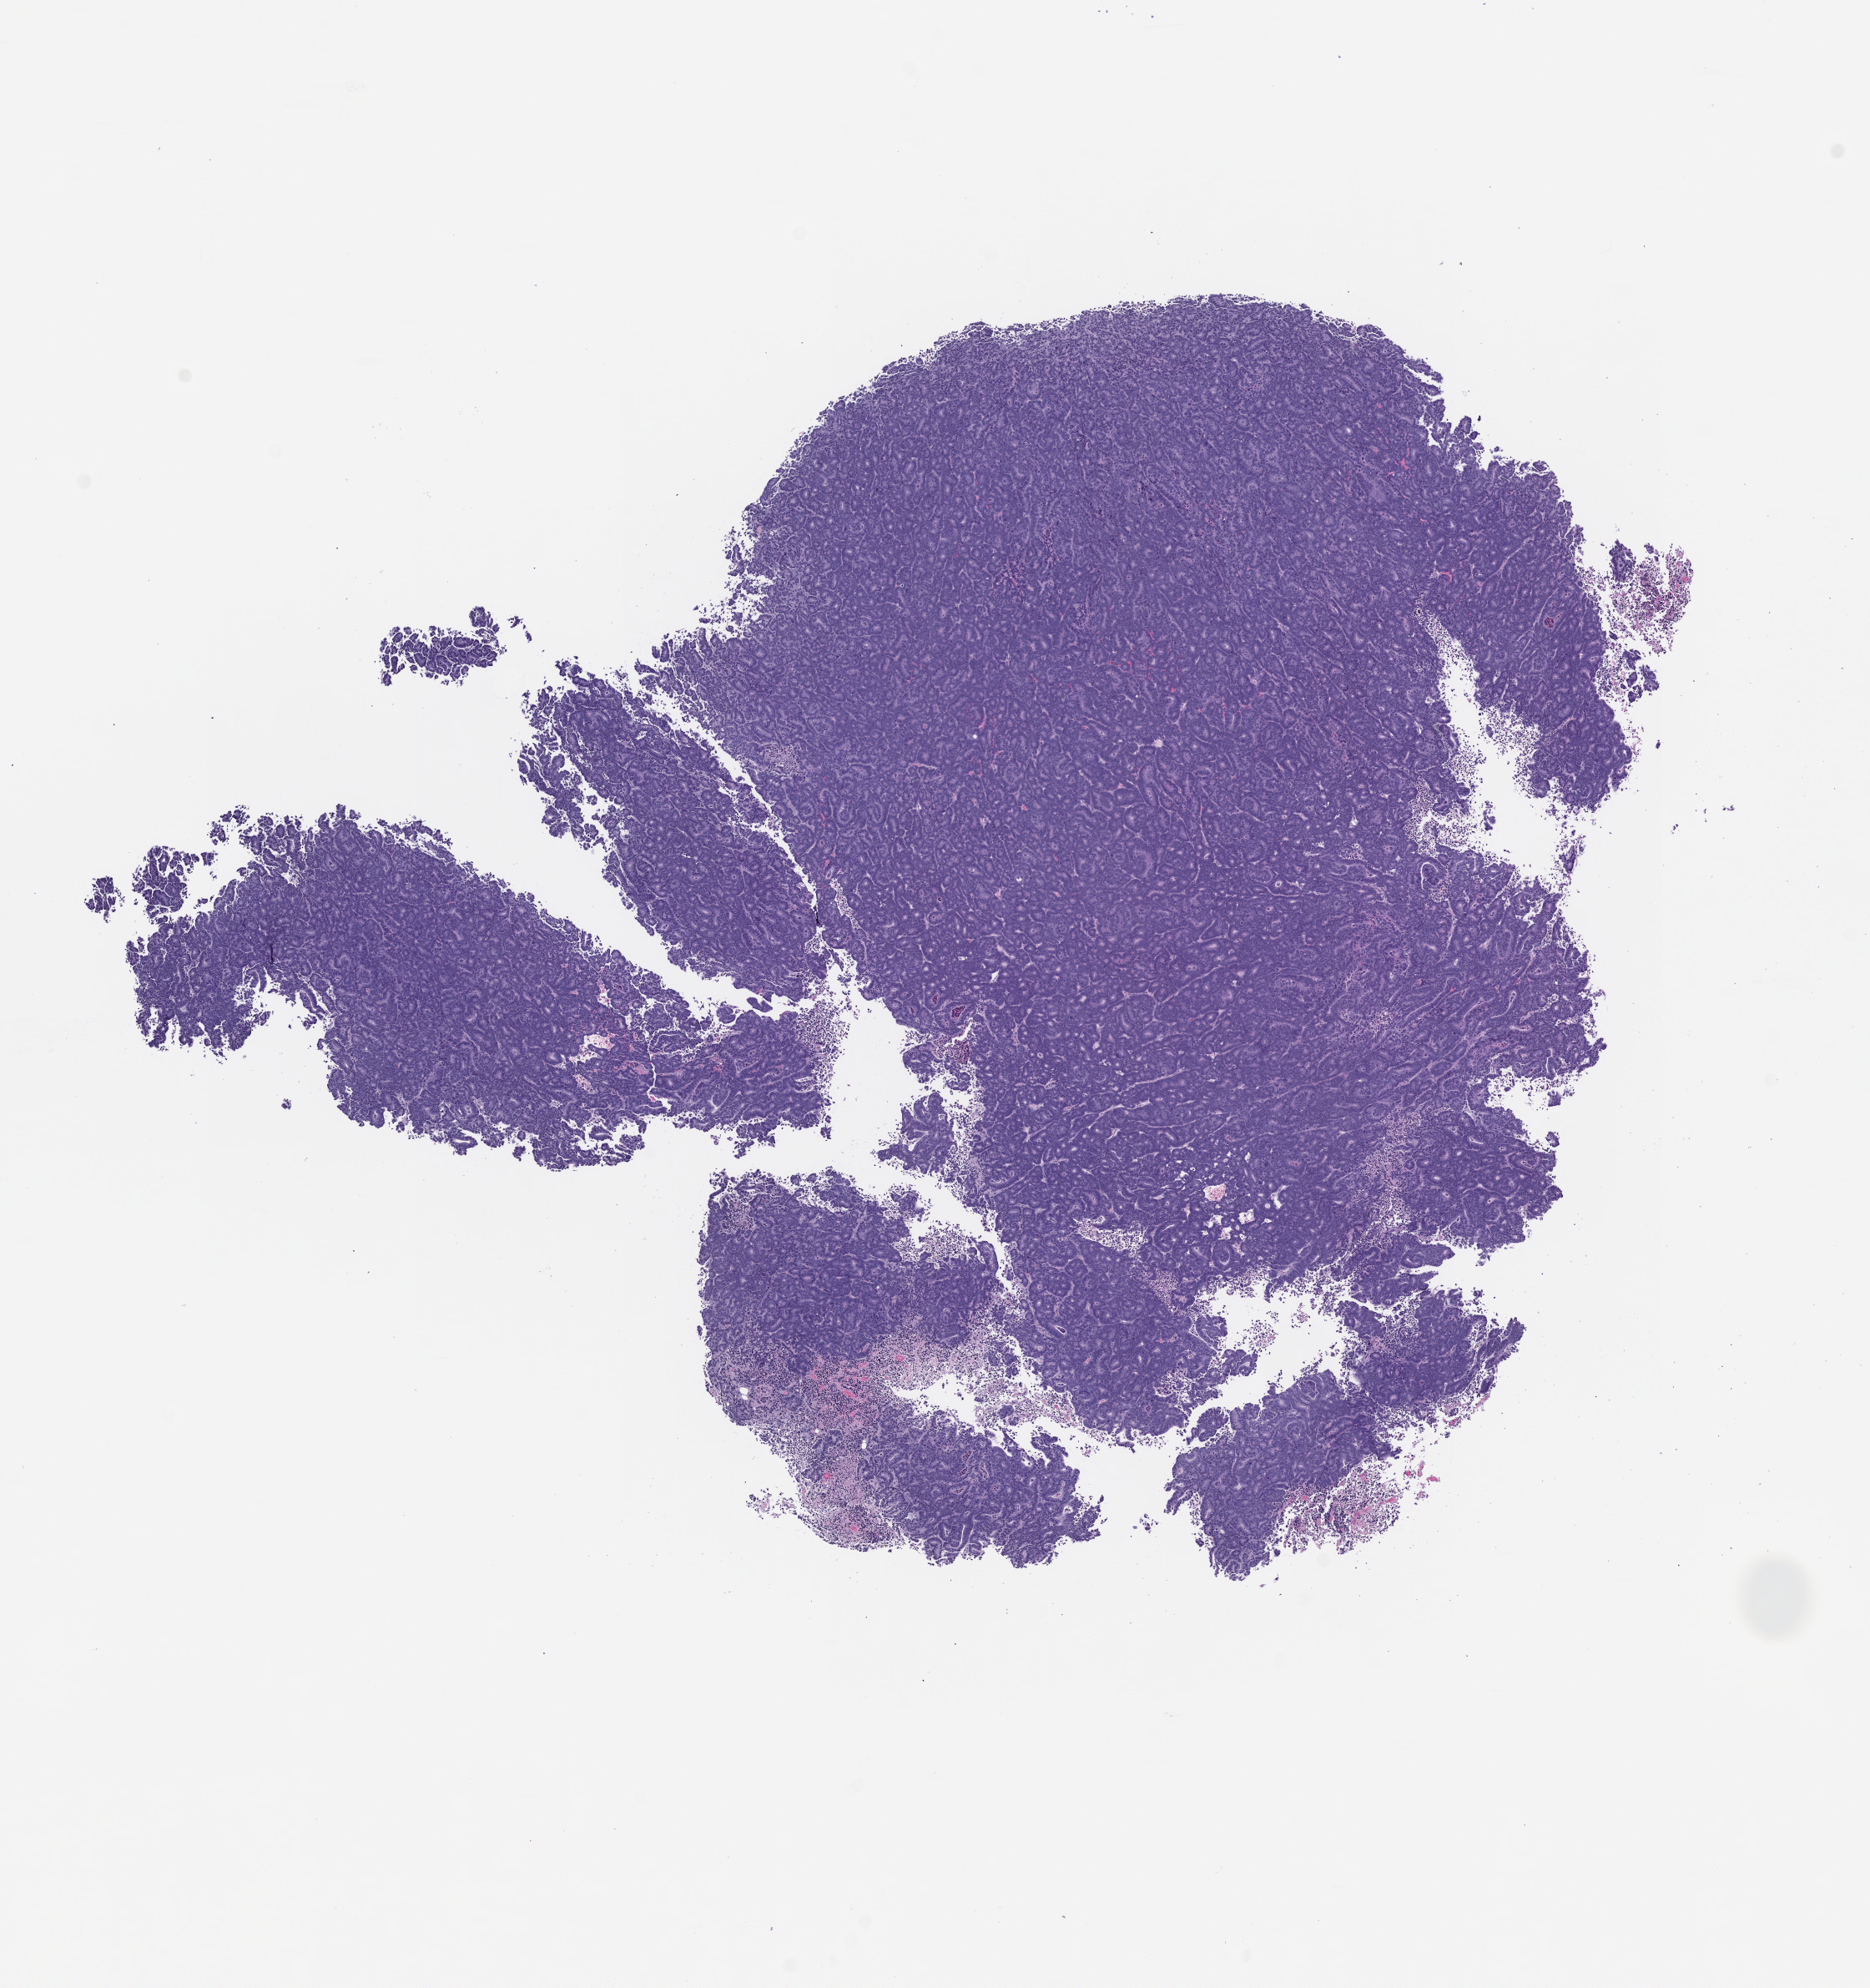
Hematoxylin and eosin (H&E) whole-slide image of a patient-derived xenograft (PDX) tumor grown in a mouse, a low-resolution overview of the entire scanned area, about 9.0 x 9.6 mm. Formalin-fixed, paraffin-embedded (FFPE) tissue. Tumor site category: small intestine.
Originating patient diagnosis: Small Intestinal Adenocarcinoma.